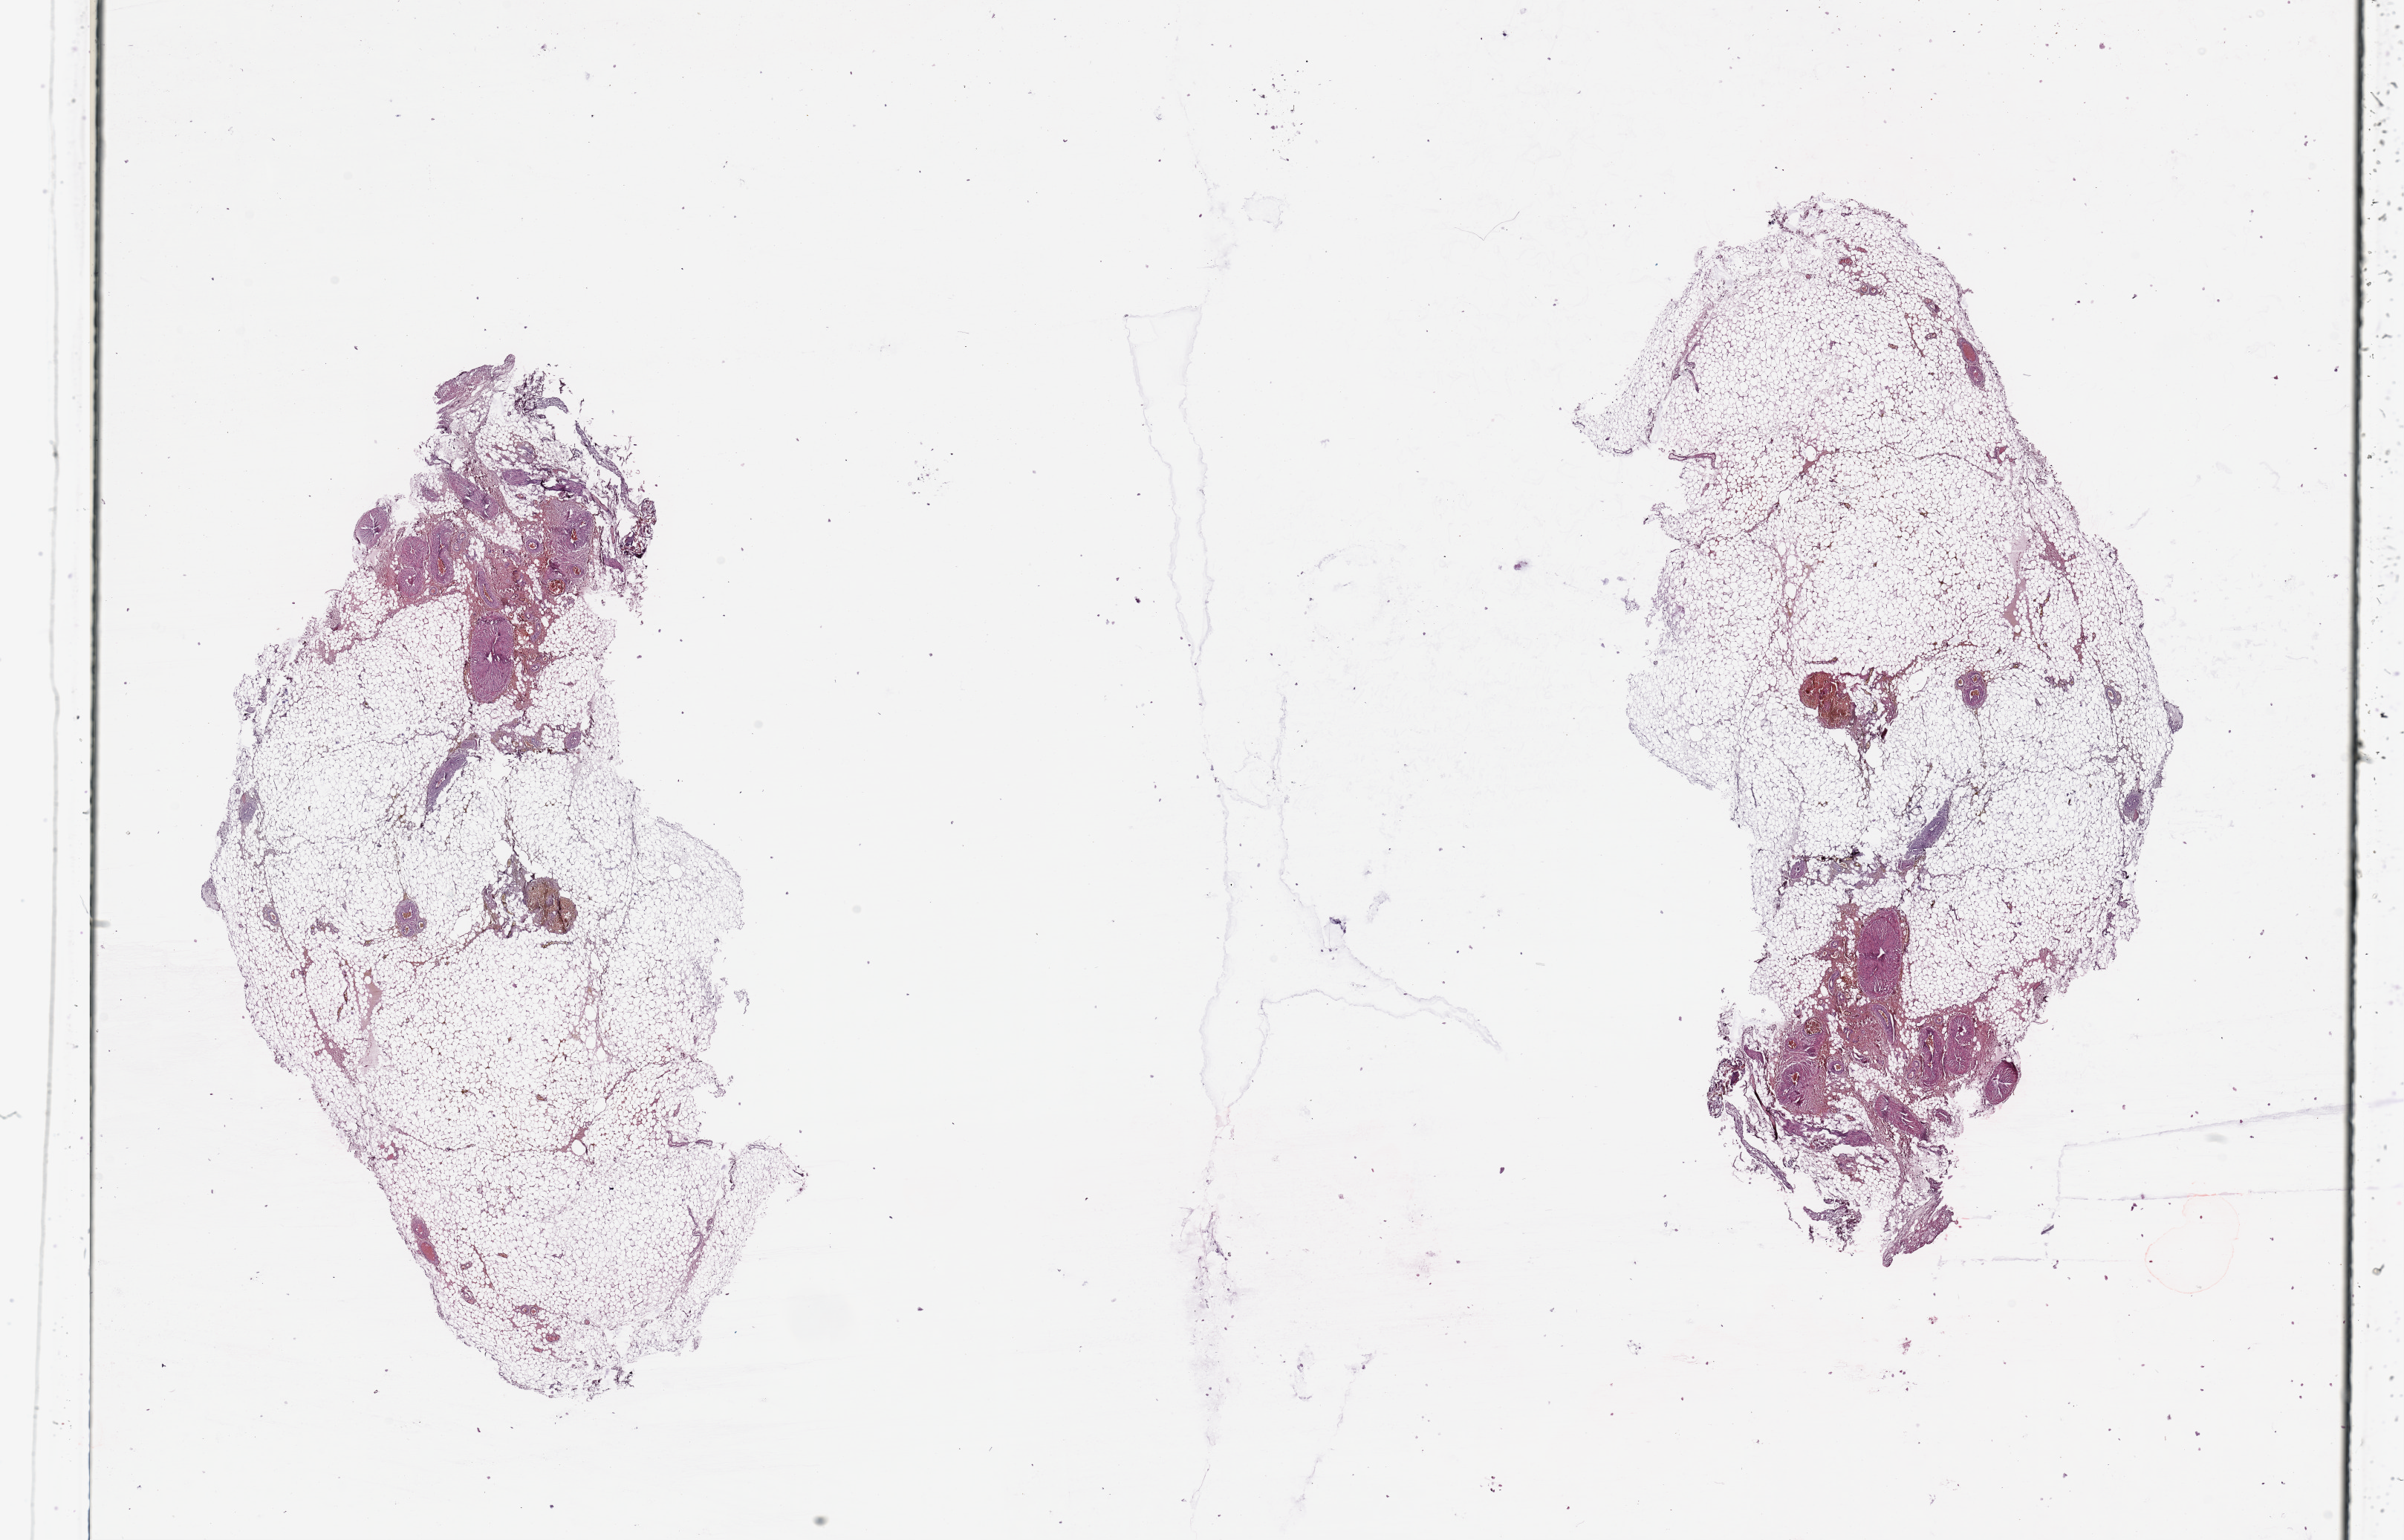
Digitized H&E tissue section (whole slide), shown as a low-resolution overview of the whole scanned area (about 25.6 x 16.4 mm). Normal (non-tumour) tissue sample, sampled site: lymph node. 46-year-old female patient.
- this section: normal (non-tumour) tissue from the same patient
- patient diagnosis: Malignant melanoma, NOS